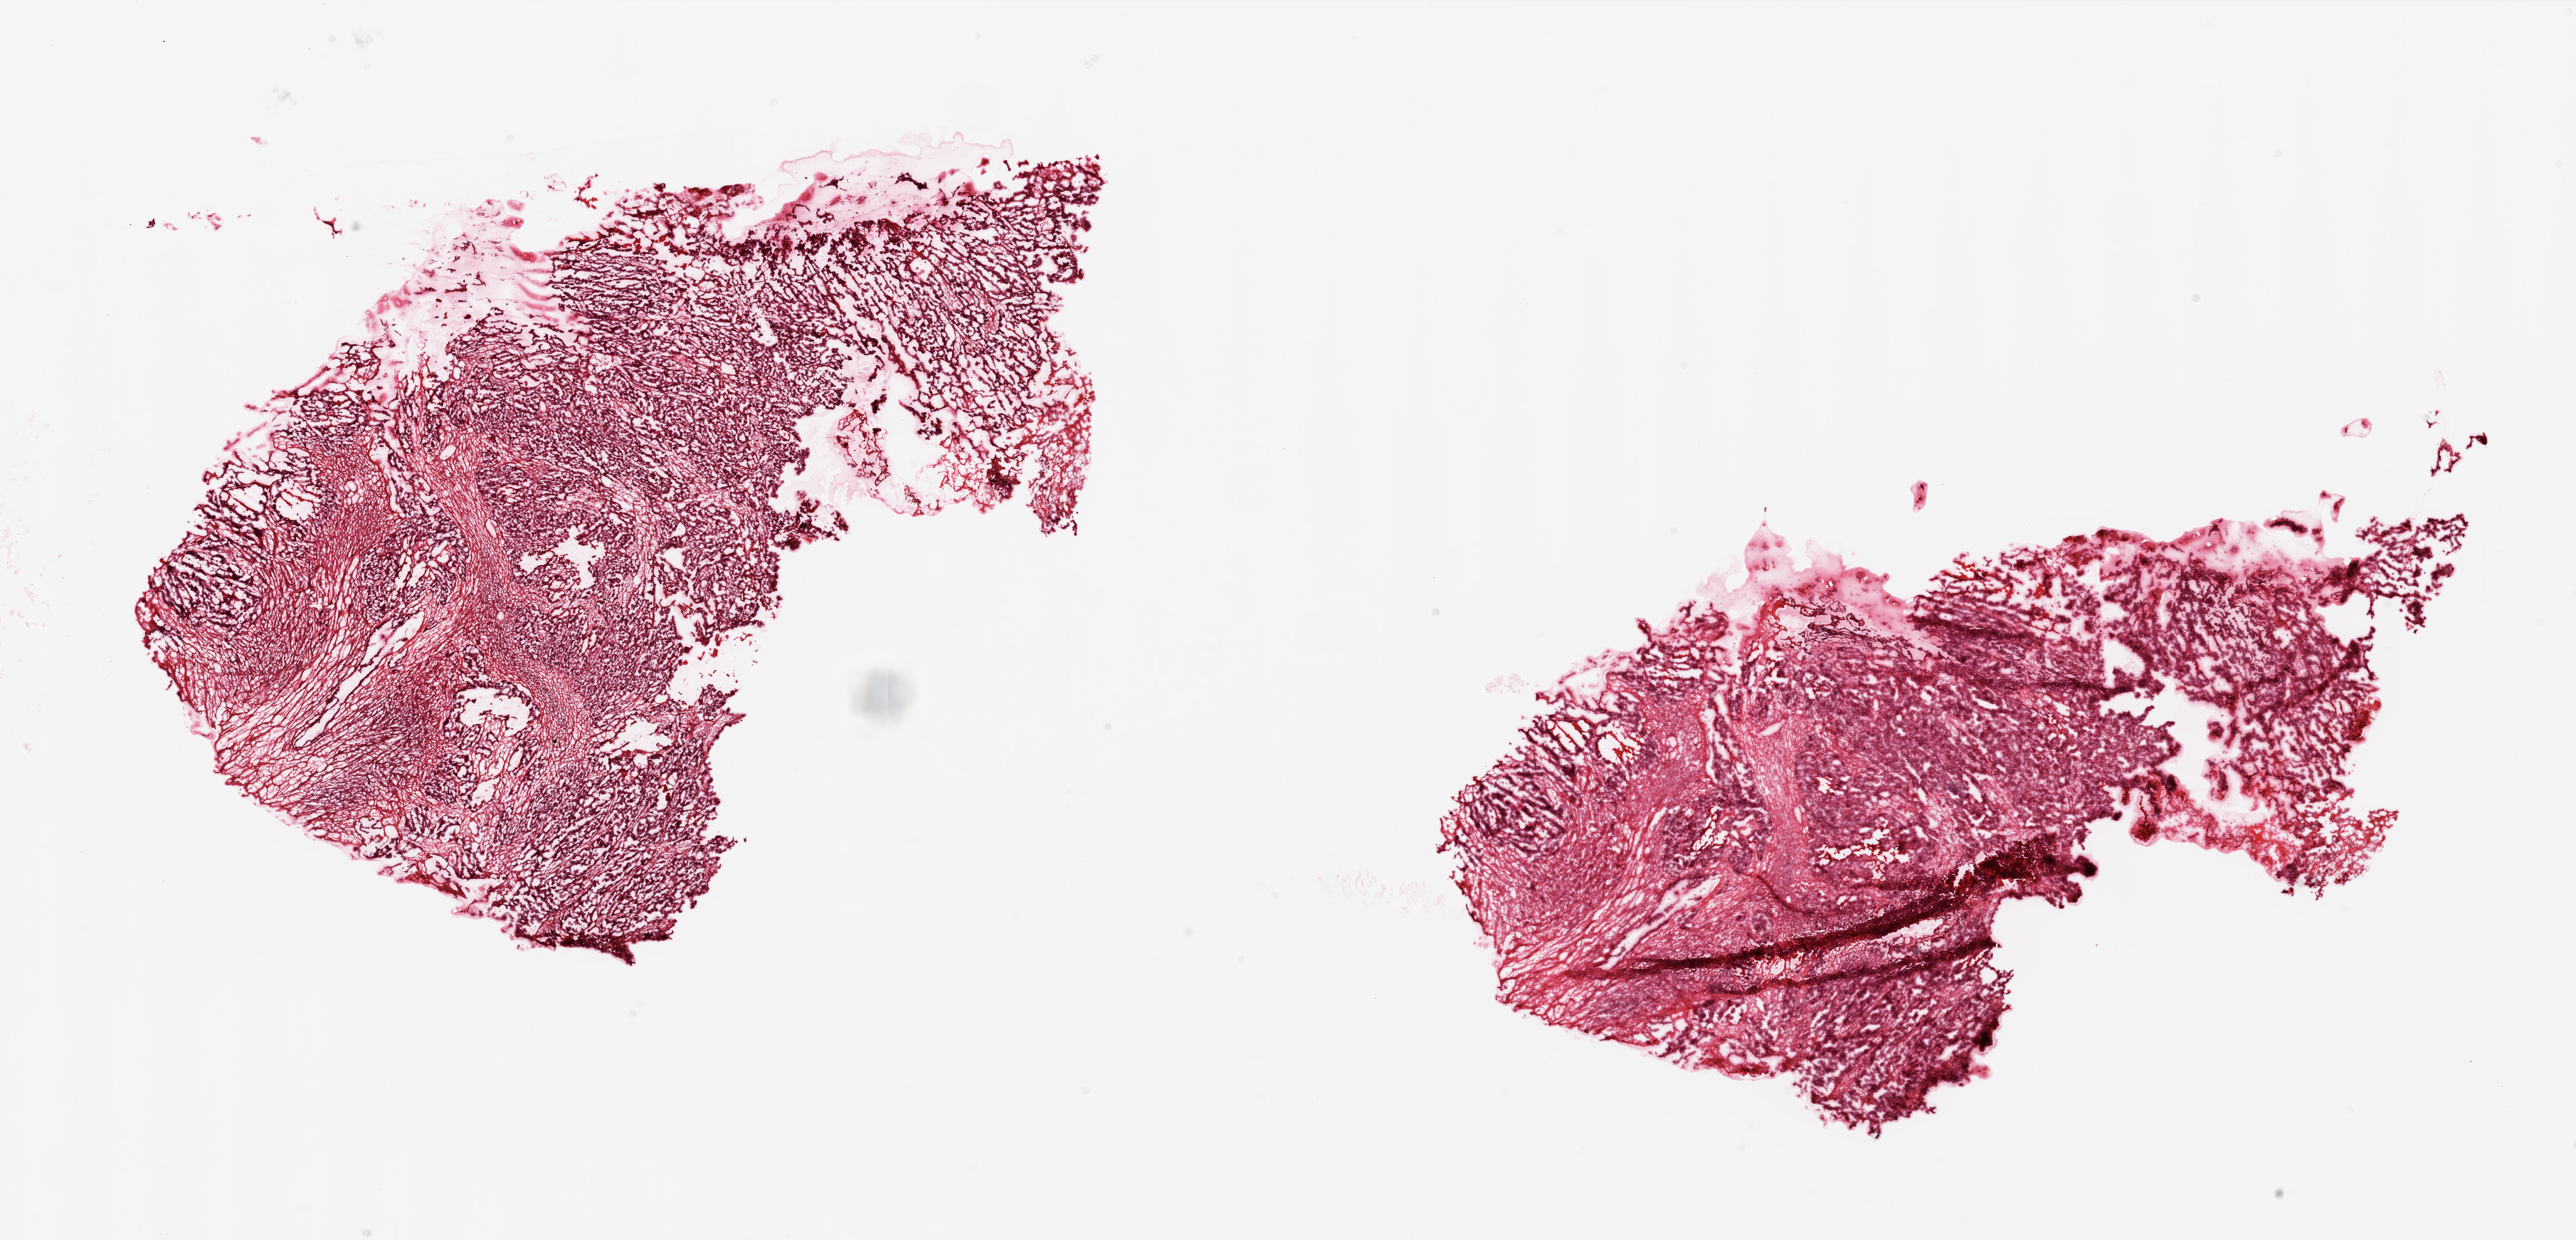
Digitized H&E tissue section (whole slide) — low-resolution overview of the scanned area, about 29.0 x 13.9 mm; frozen section from the top of the tissue portion; primary tumour sample from the ovary. Patient: female, age at initial diagnosis 77 years. Histologic grade: G3 (poorly differentiated). Pathologist review of this section (percent, as recorded): tumour cells 75%, tumour nuclei 85%, normal cells 0%, stromal cells 25%, necrosis 0%.
• FIGO stage: IIIC
• laterality: bilateral
• pathologic diagnosis: Serous cystadenocarcinoma, NOS